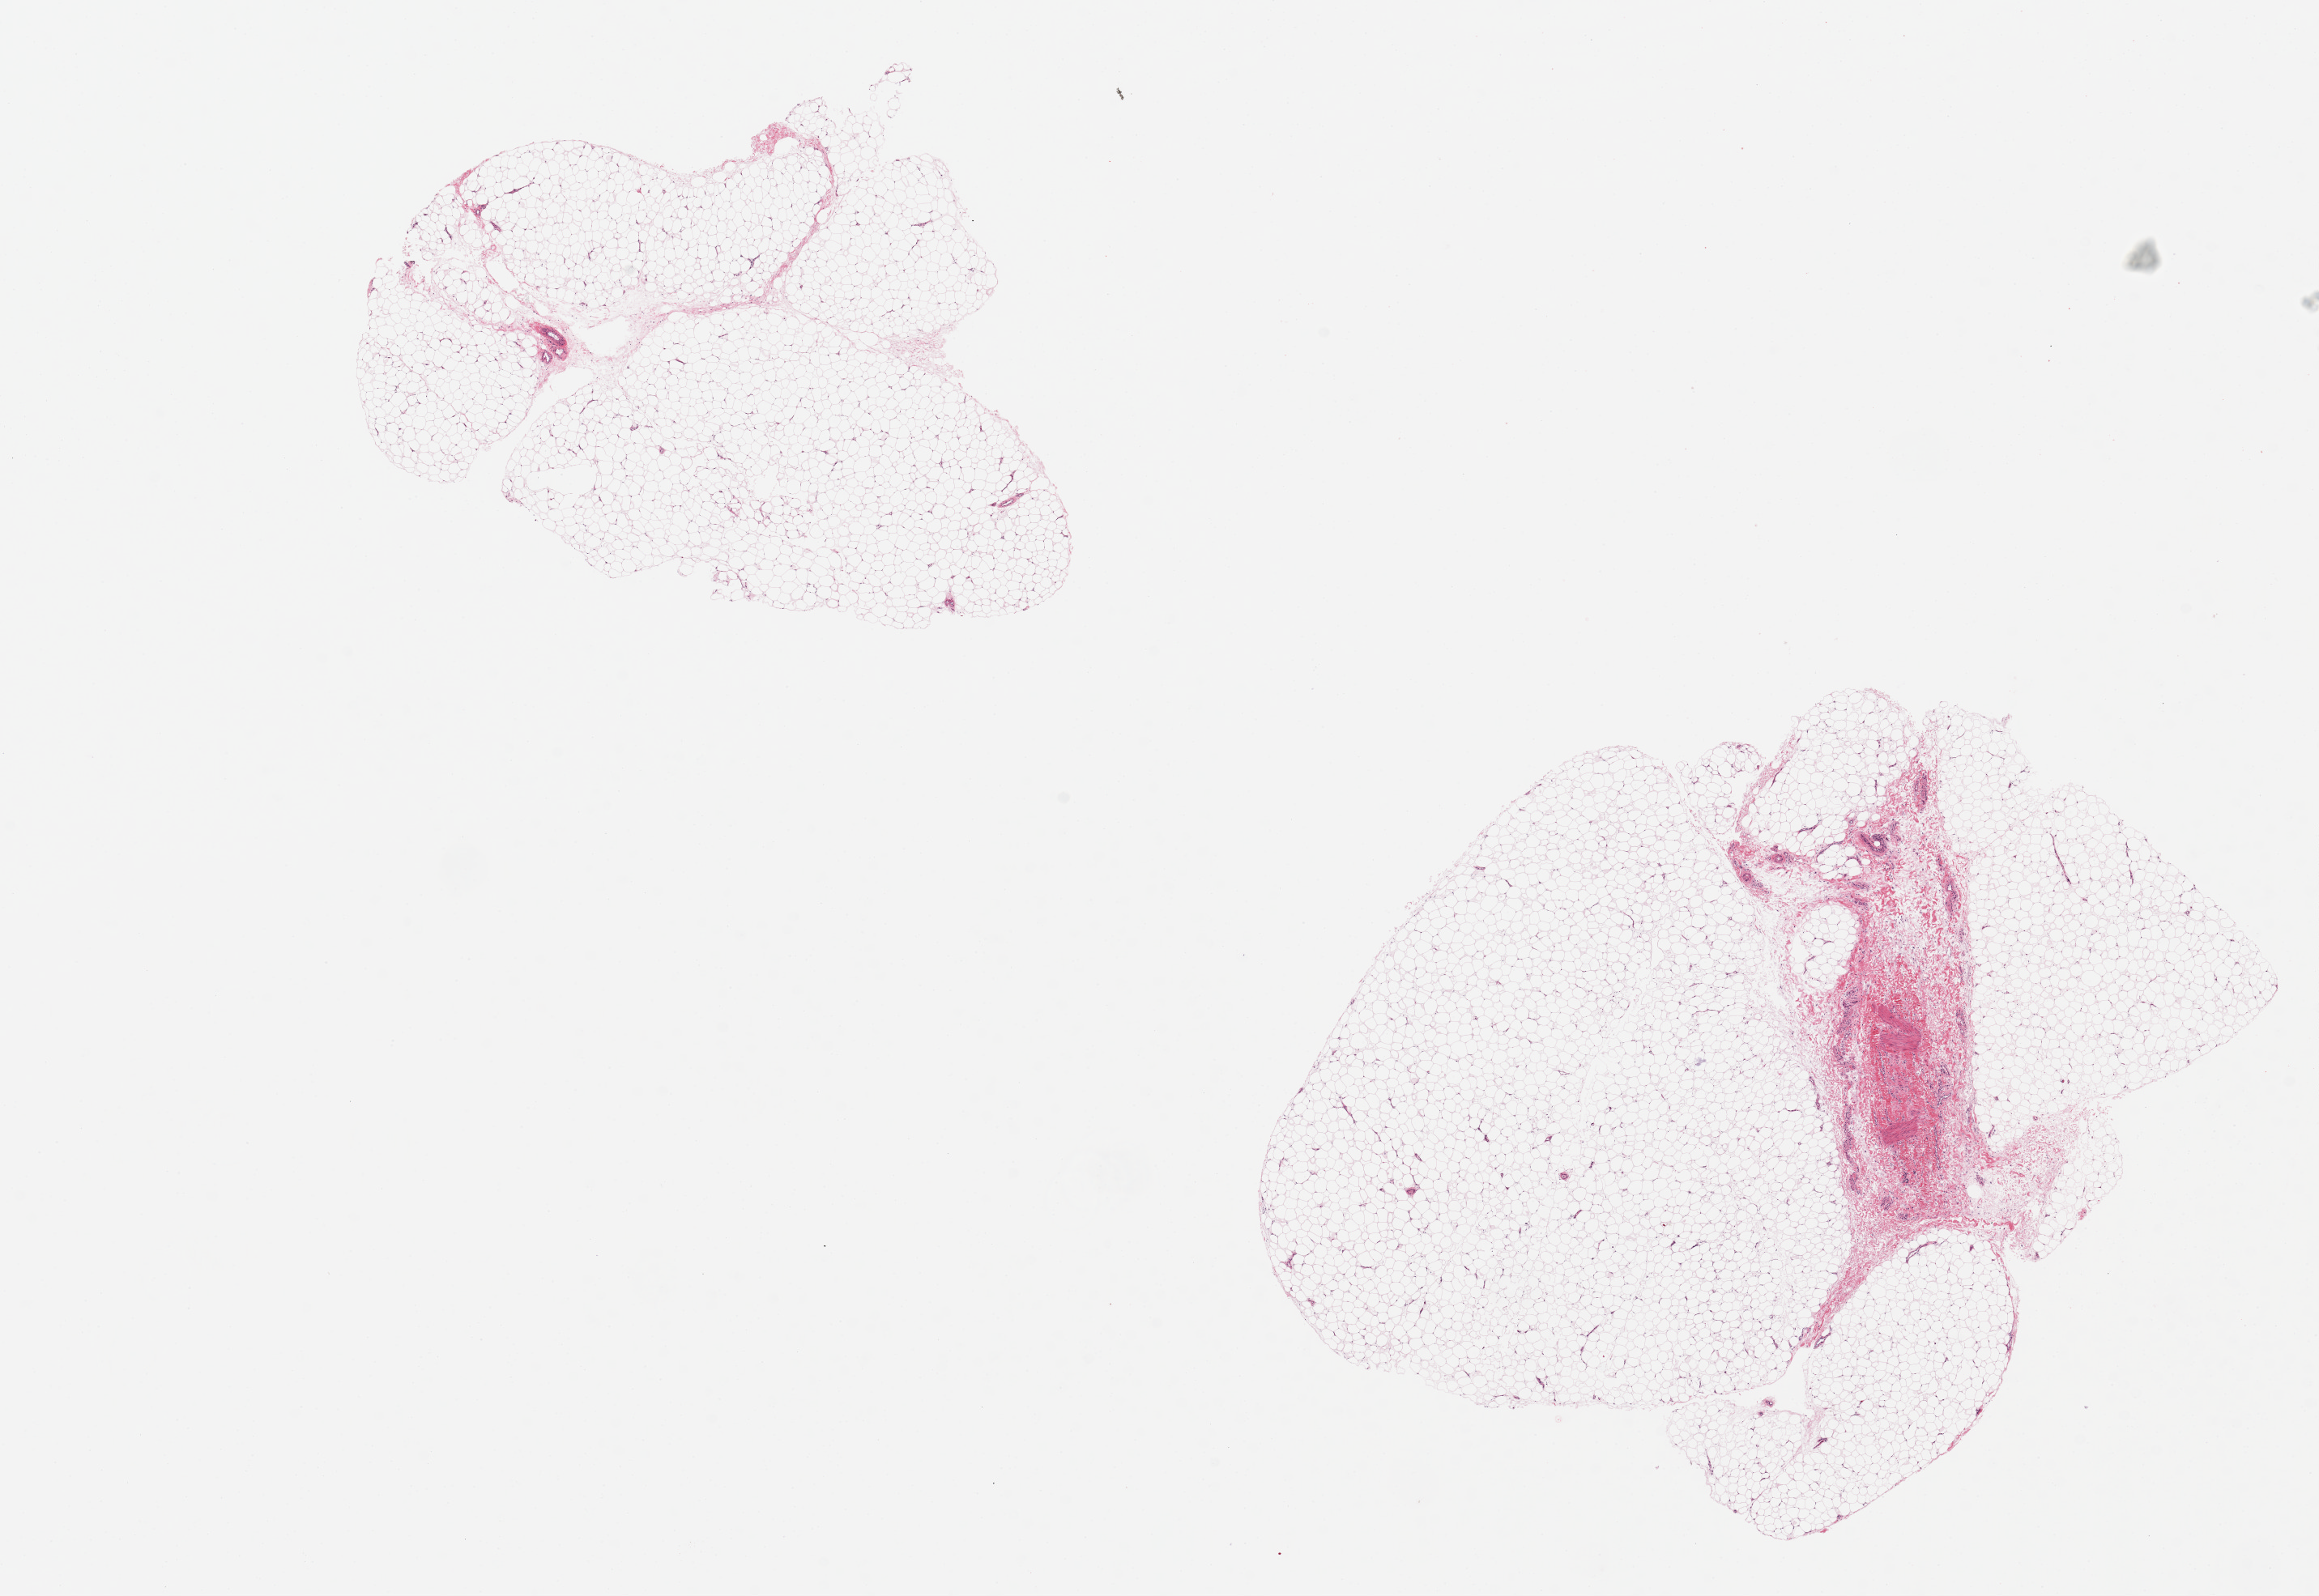
Whole-slide image, hematoxylin and eosin (H&E) stain — whole scanned area (about 22.6 x 15.6 mm, acquisition: 20x scan) shown as a low-resolution overview. PAXgene-fixed, paraffin-embedded tissue. Section of adipose tissue (target tissue). Donor tissue sample. Male donor.
Review note (as recorded): 2 pieces~7x7mm.